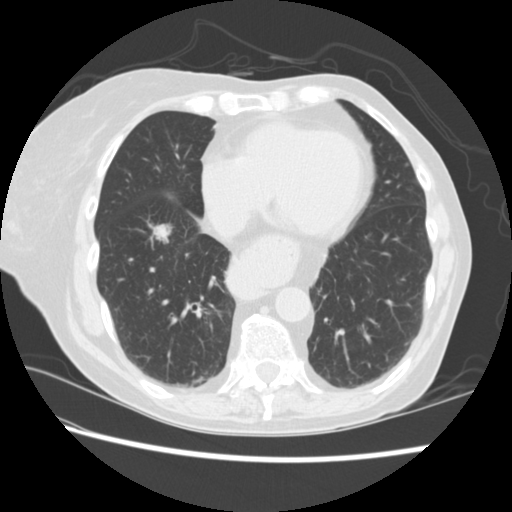
Low-dose screening chest CT, one axial slice; position 70 of 224 along the scan axis; lung window (W 1500 / L -600 HU); 512 × 512 image matrix.
Annotated regions visible in this slice (expert manual segmentation):
- lesion 2 (tumor, lower lobe of right lung): box from (x=152, y=224) to (x=171, y=242) px